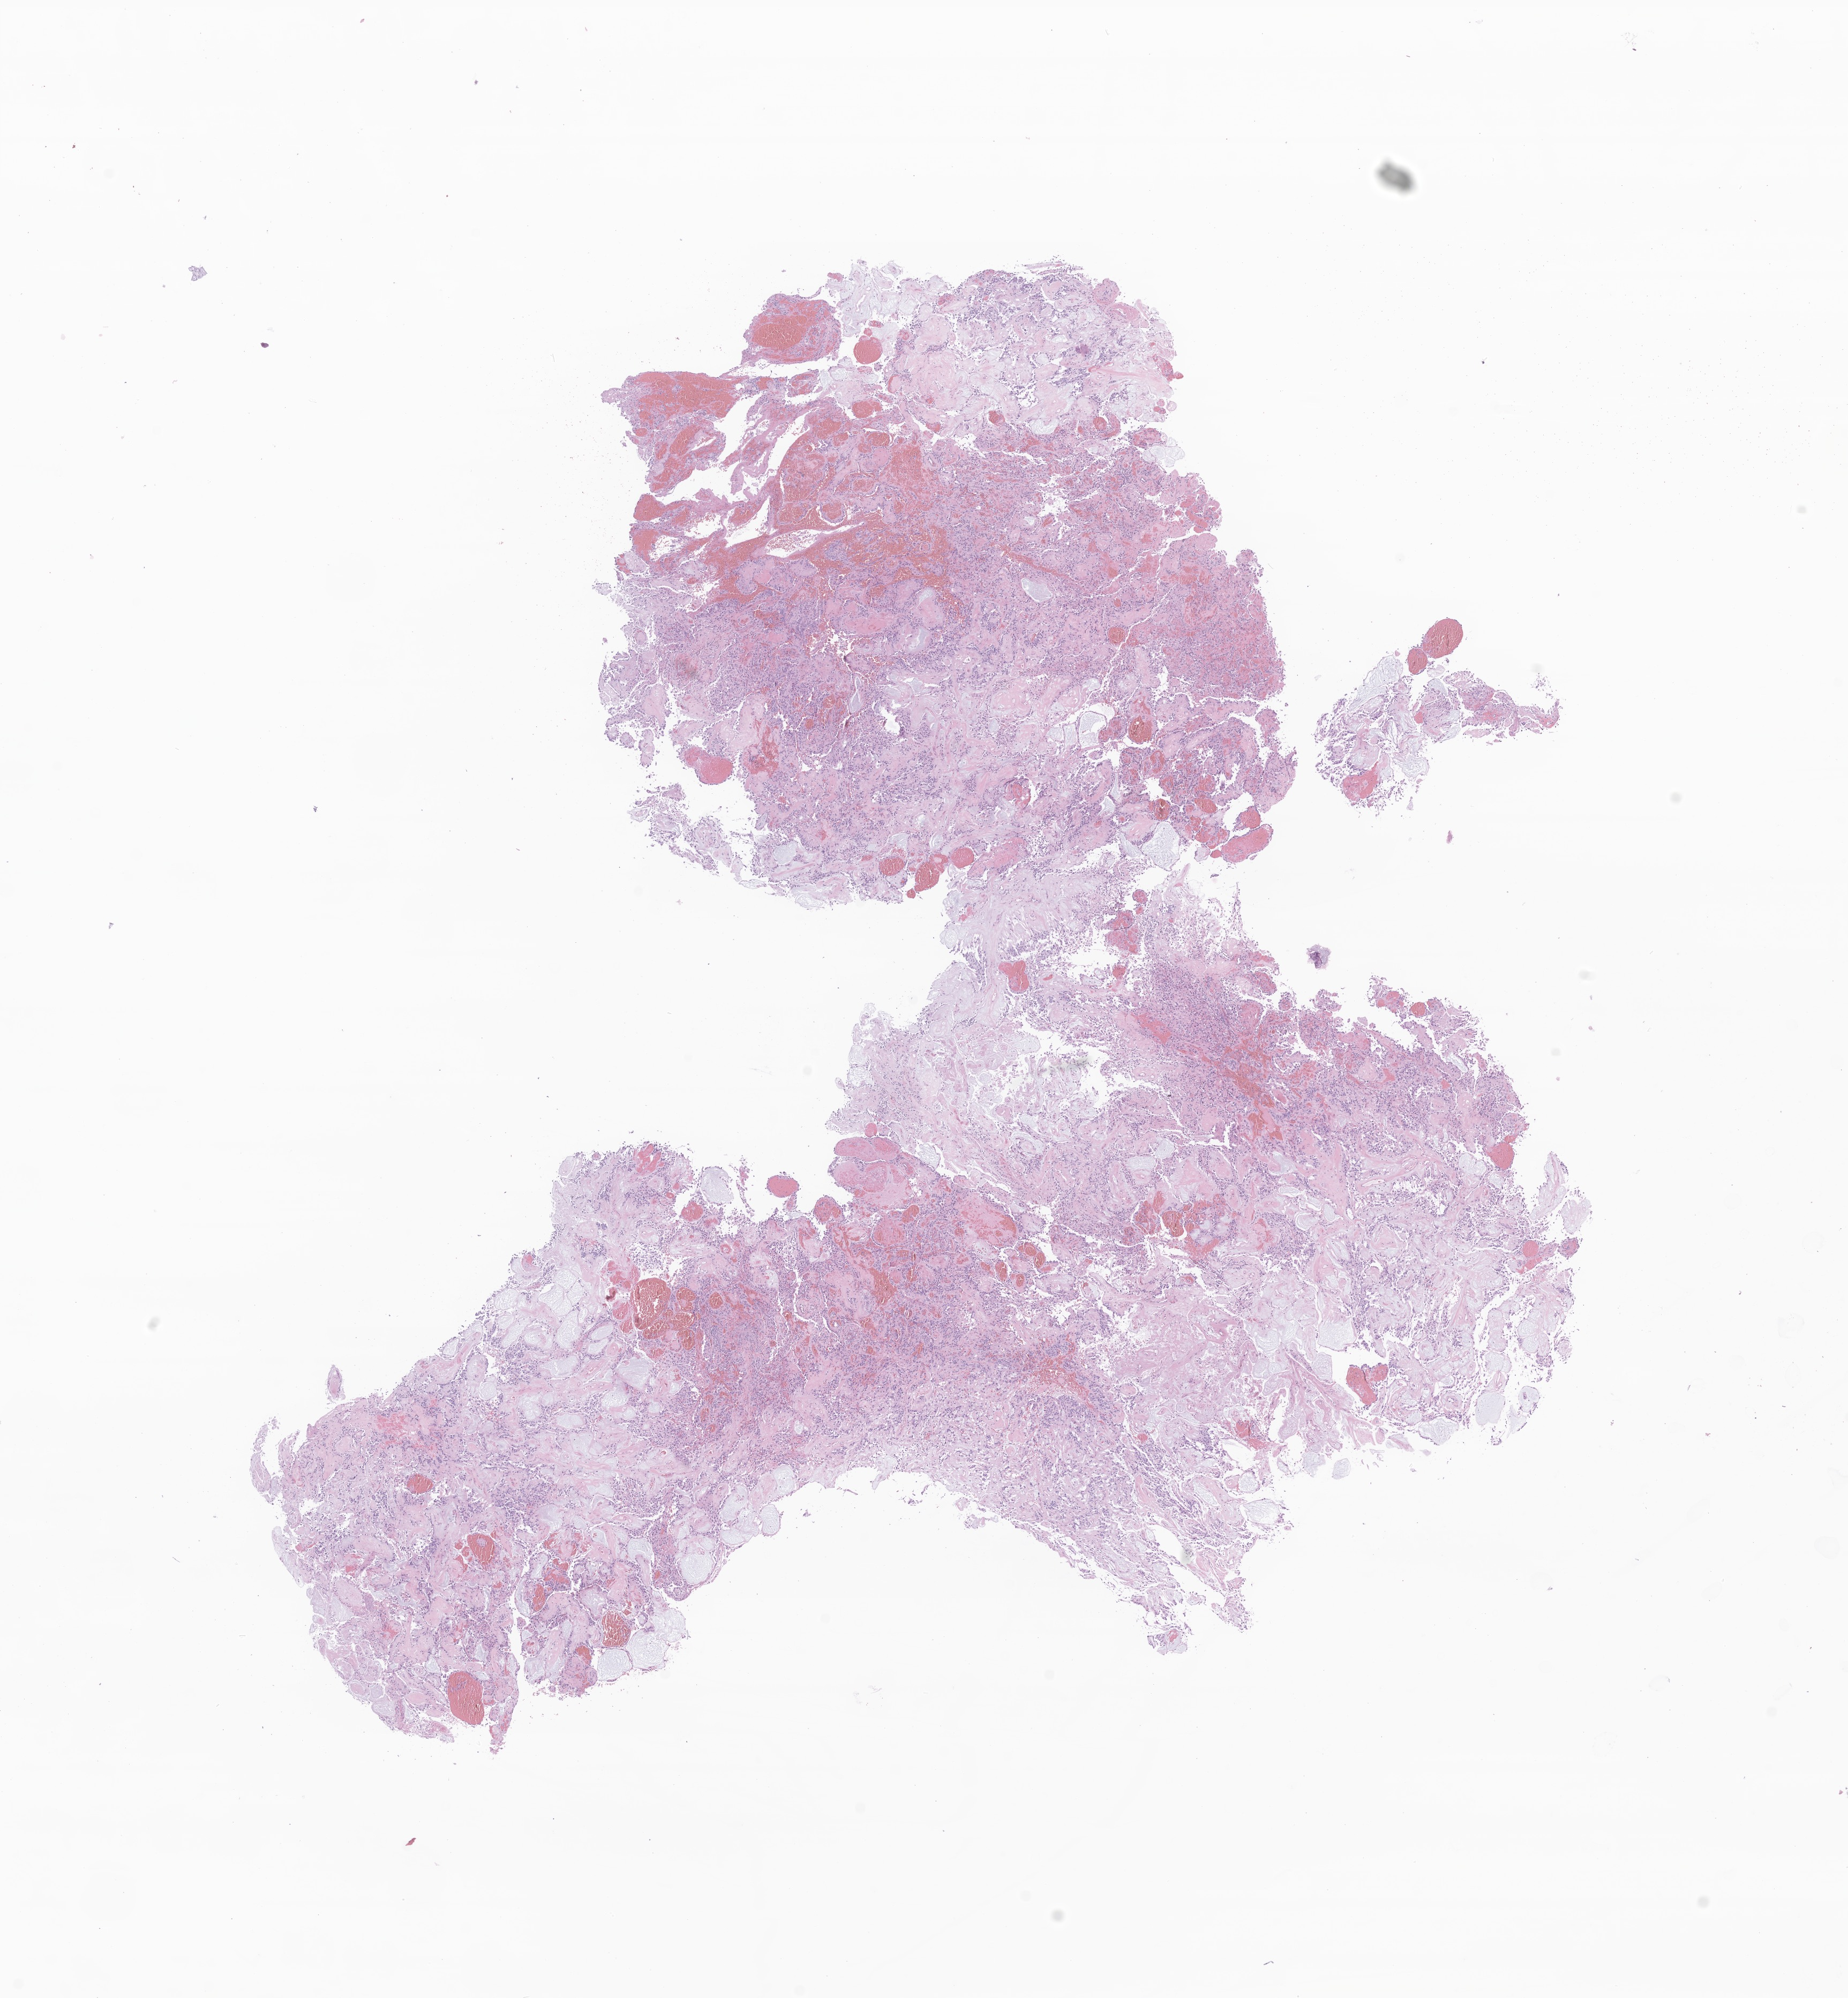
Digitized haematoxylin and eosin-stained section of tumor tissue from the spinal cord, low-resolution overview of the scanned area, about 14.5 x 15.7 mm; formalin-fixed paraffin-embedded section. Patient male; age 228 months (19 years).
Diagnosis (ICD-O-3 morphology term): Myxopapillary ependymoma.